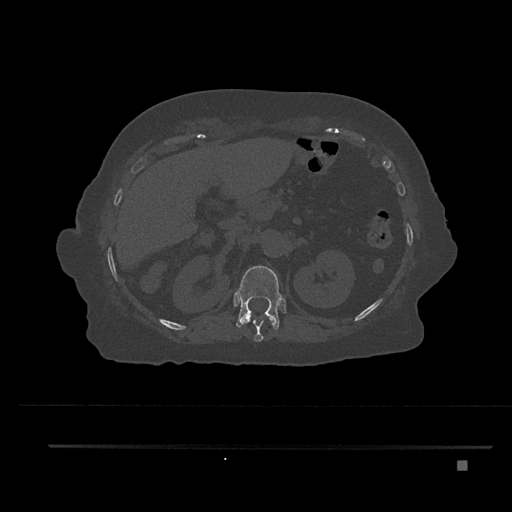
CT including the spine, one axial slice. Slice 279 of 797 in the series (ordered by position). Reconstruction kernel Br40s/3. Bone window (W 1800 / L 400 HU). 0.5 mm slice thickness. 512 × 512 image matrix, field of view 437 × 437 mm. Female patient, age 76 years. From the clinical record (not read from this slice): primary cancer: lung.
Outlined on this slice (semi-automatic segmentation, software-assisted and operator-edited):
- T11 vertebra: bounding box [x1, y1, x2, y2] px = [241, 313, 275, 342]
- T12 vertebra: [235, 266, 282, 330]